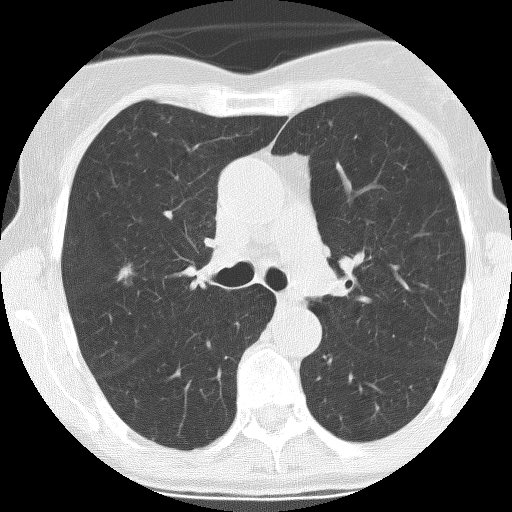
Chest CT (low-dose screening protocol), one axial image, baseline annual screen, lung window (W 1500 / L -600 HU), 2.5 mm slice thickness, lung (sharp) reconstruction kernel (BONE), slice 92 of 261 in the series. Female participant, aged 68 years at enrolment.
- Expert reader's lesion annotation, bounding box [x1, y1, x2, y2] px = [102, 251, 143, 295].
- Reader record for this screening exam (exam-level; its link to the box is not recorded): non-calcified nodule or mass ≥4 mm, right upper lobe, 13 × 8 mm, spiculated (stellate) margins, mixed attenuation.
- Later outcome: lung cancer diagnosed 113 days after this screen — adenocarcinoma, NOS, right upper lobe, moderately differentiated (G2), stage IA (AJCC 6th edition), 10 mm at pathology.